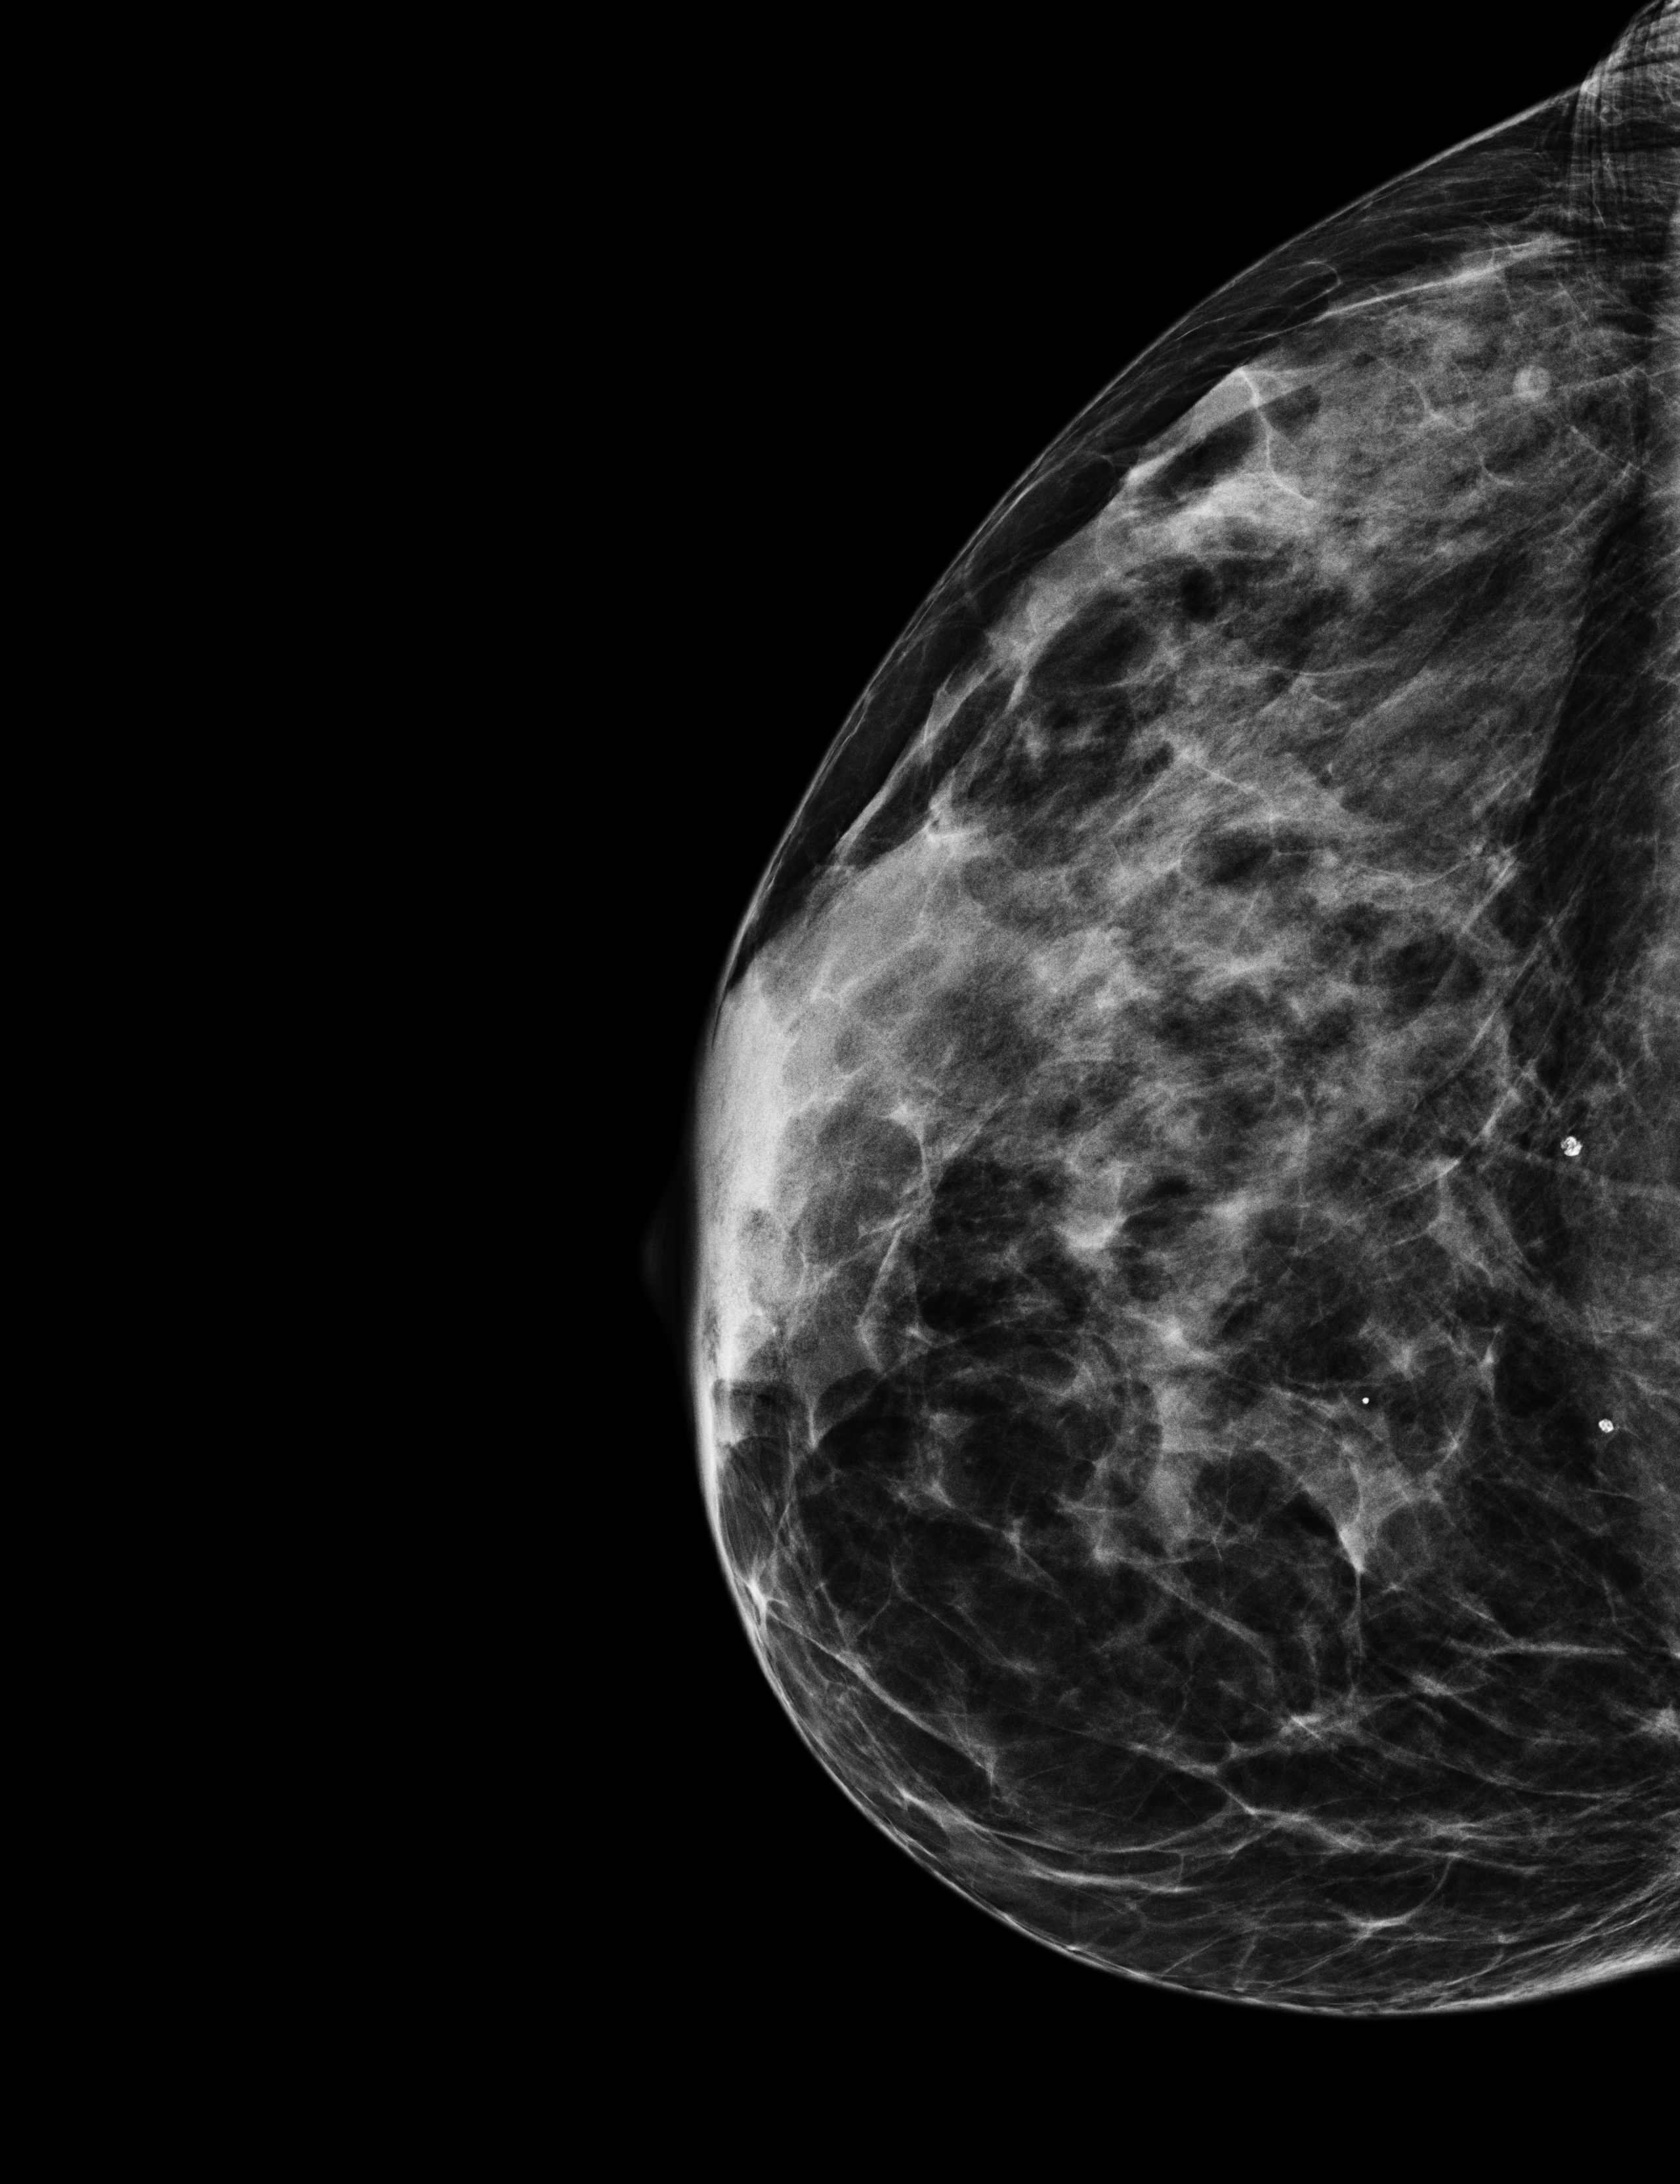
Screening examination, compressed breast thickness 32 mm. Patient: female, 54 years.
Image type: full-field digital mammogram. Breast: right. Projection: CC view.